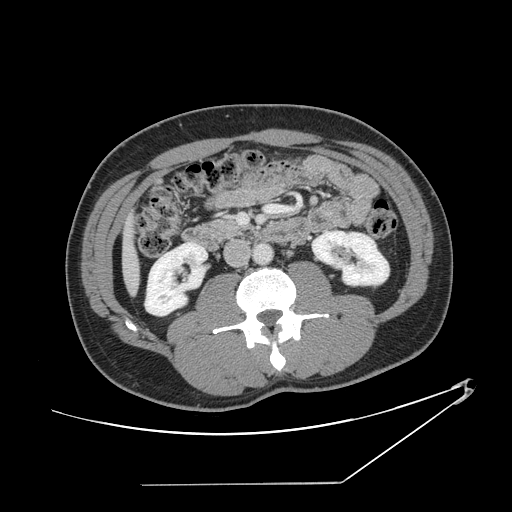
Contrast-enhanced abdominal CT, one axial slice. Position 44 of 152 along the scan axis. 120 kVp. Intravenous contrast given. Soft-tissue window (W 400 / L 40 HU). 2.5 mm slice thickness. 512 × 512 image matrix. Male patient, age 45 years. Case-level facts recorded for this patient, not image findings: diagnosis: colorectal cancer liver metastases, imaged before liver resection; multiple liver metastases: no; largest metastasis: 1 cm; chemotherapy before resection: yes.
Outlined on this slice (manually delineated by an expert):
- liver: bounding box [x1, y1, x2, y2] px = [124, 229, 139, 291]
- planned liver remnant (the part of the liver to remain after resection): [124, 229, 139, 291]